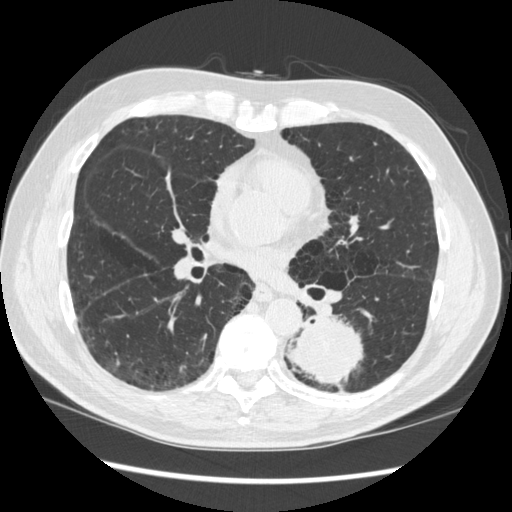
Low-dose screening chest CT, axial slice. First (baseline) screen. Lung window (W 1500 / L -600 HU). 1.25 mm slice thickness. Slice 158 of 348 in the series. Male participant, aged 72 years at enrolment.
Expert reader's lesion annotation, box from (x=266, y=304) to (x=370, y=396) px. The screening reader recorded 2 non-calcified nodules or masses ≥4 mm on this exam; which of them this box marks is not recorded. Official screen result: positive, change unspecified: nodule(s) >= 4 mm or enlarging nodule(s), mass(es), or other non-specific abnormalities suspicious for lung cancer. Participant outcome: lung cancer diagnosed 37 days after this screen — squamous cell carcinoma, NOS, left lower lobe, stage IIIA (AJCC 6th edition), 60 mm at pathology.